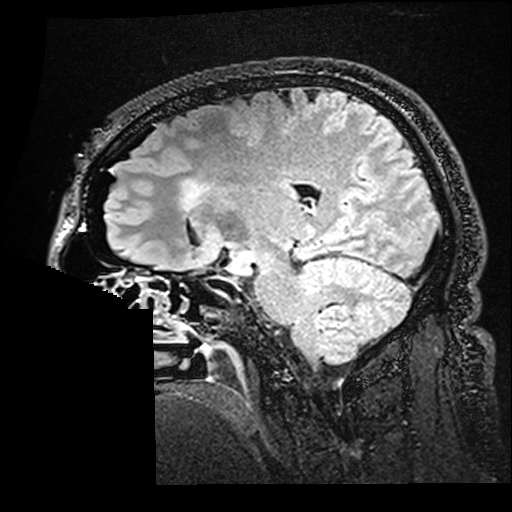
Brain MRI from a brain-tumour surgery series, one sagittal slice. Slice 106 of 176 in the series (ordered by position). T2 FLAIR. 512 × 512 image matrix, field of view 250 × 250 mm. From the clinical record (not read from this slice): histopathology: Astrocytoma; WHO grade: 2; IDH mutation: yes; tumour location: Right Insular.
Outlined on this slice (outlined manually by an expert reader):
- residual tumour: bounding box <184,182,208,208> (left, top, right, bottom; pixels)